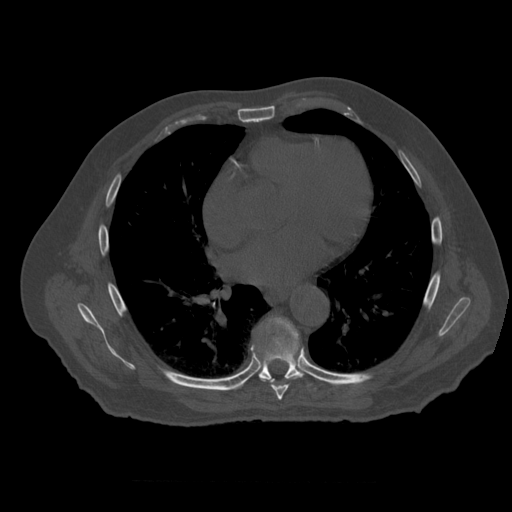
CT including the spine, one axial slice. Slice 351 of 399 in the series (ordered by position). Reconstruction kernel STANDARD. 120 kVp. Bone window (W 1800 / L 400 HU). 1.25 mm slice thickness. 512 × 512 image matrix, field of view 407 × 407 mm. Patient age 73 years. From the clinical record (not read from this slice): primary cancer: prostate; vertebrae with lytic lesions (as recorded): L2.
Annotated regions visible in this slice (semi-automatic segmentation, software-assisted and operator-edited):
- T7 vertebra: bounding box [x1, y1, x2, y2] px = [261, 375, 304, 400]
- T8 vertebra: [251, 317, 311, 387]